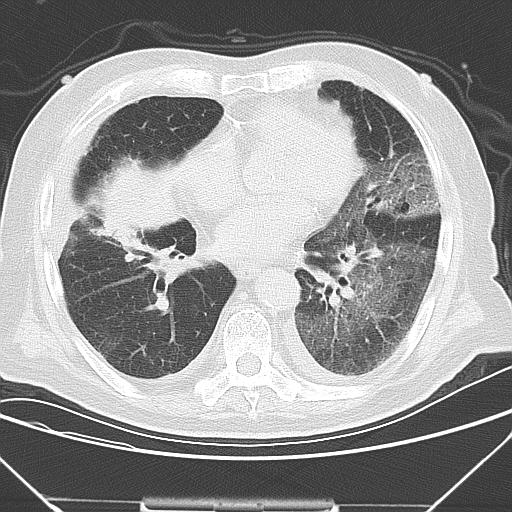
Chest CT, one axial slice; slice 13 of 43 in the series (ordered by position); 120 kVp; lung window (W 1500 / L -600 HU); 5 mm slice thickness; 512 × 512 image matrix, field of view 343 × 343 mm. Patient: male, 85 years. Case-level facts recorded for this patient, not image findings: clinical TNM (as recorded): T4 N3 M2.
Structures marked on this image (bounding box drawn by a radiologist):
- lung tumour (recorded histology: squamous cell carcinoma): box from (x=97, y=153) to (x=175, y=253) px